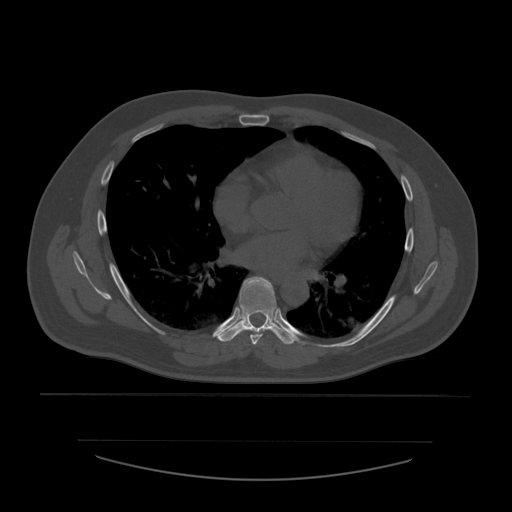
CT including the spine, one axial slice; position 366 of 532 along the scan axis; reconstruction kernel STANDARD; 120 kVp; bone window (W 1800 / L 400 HU); 1.25 mm slice thickness; 512 × 512 image matrix. Patient age 44 years. Case-level facts recorded for this patient, not image findings: primary cancer: soft tissue sarcoma.
Structures marked on this image (semi-automatically segmented with operator editing):
- T6 vertebra: bounding box [x1, y1, x2, y2] px = [250, 280, 275, 345]
- T7 vertebra: [217, 277, 295, 345]